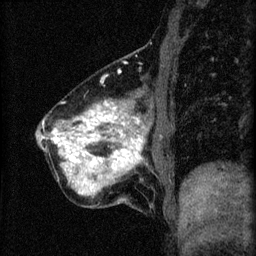
Breast MRI (dynamic contrast-enhanced), one sagittal slice. Position 17 of 60 along the scan axis. 3 images stored at this slice position (order not interpretable as contrast timing). 1.5 T. TE 4.2 ms, TR 8.2 ms. 256 × 256 image matrix, field of view 180 × 180 mm. Patient: female, 40 years.
Annotated regions visible in this slice (semi-automatically segmented with operator editing):
- analysis volume of interest (the breast-tissue region the enhancement analysis was run in; not a lesion): bounding box (x1, y1, x2, y2) in pixels: (38, 88, 171, 209)
- tumour enhancement mask (voxels above the 70 % enhancement threshold inside the analysis volume of interest): (52, 104, 143, 195)